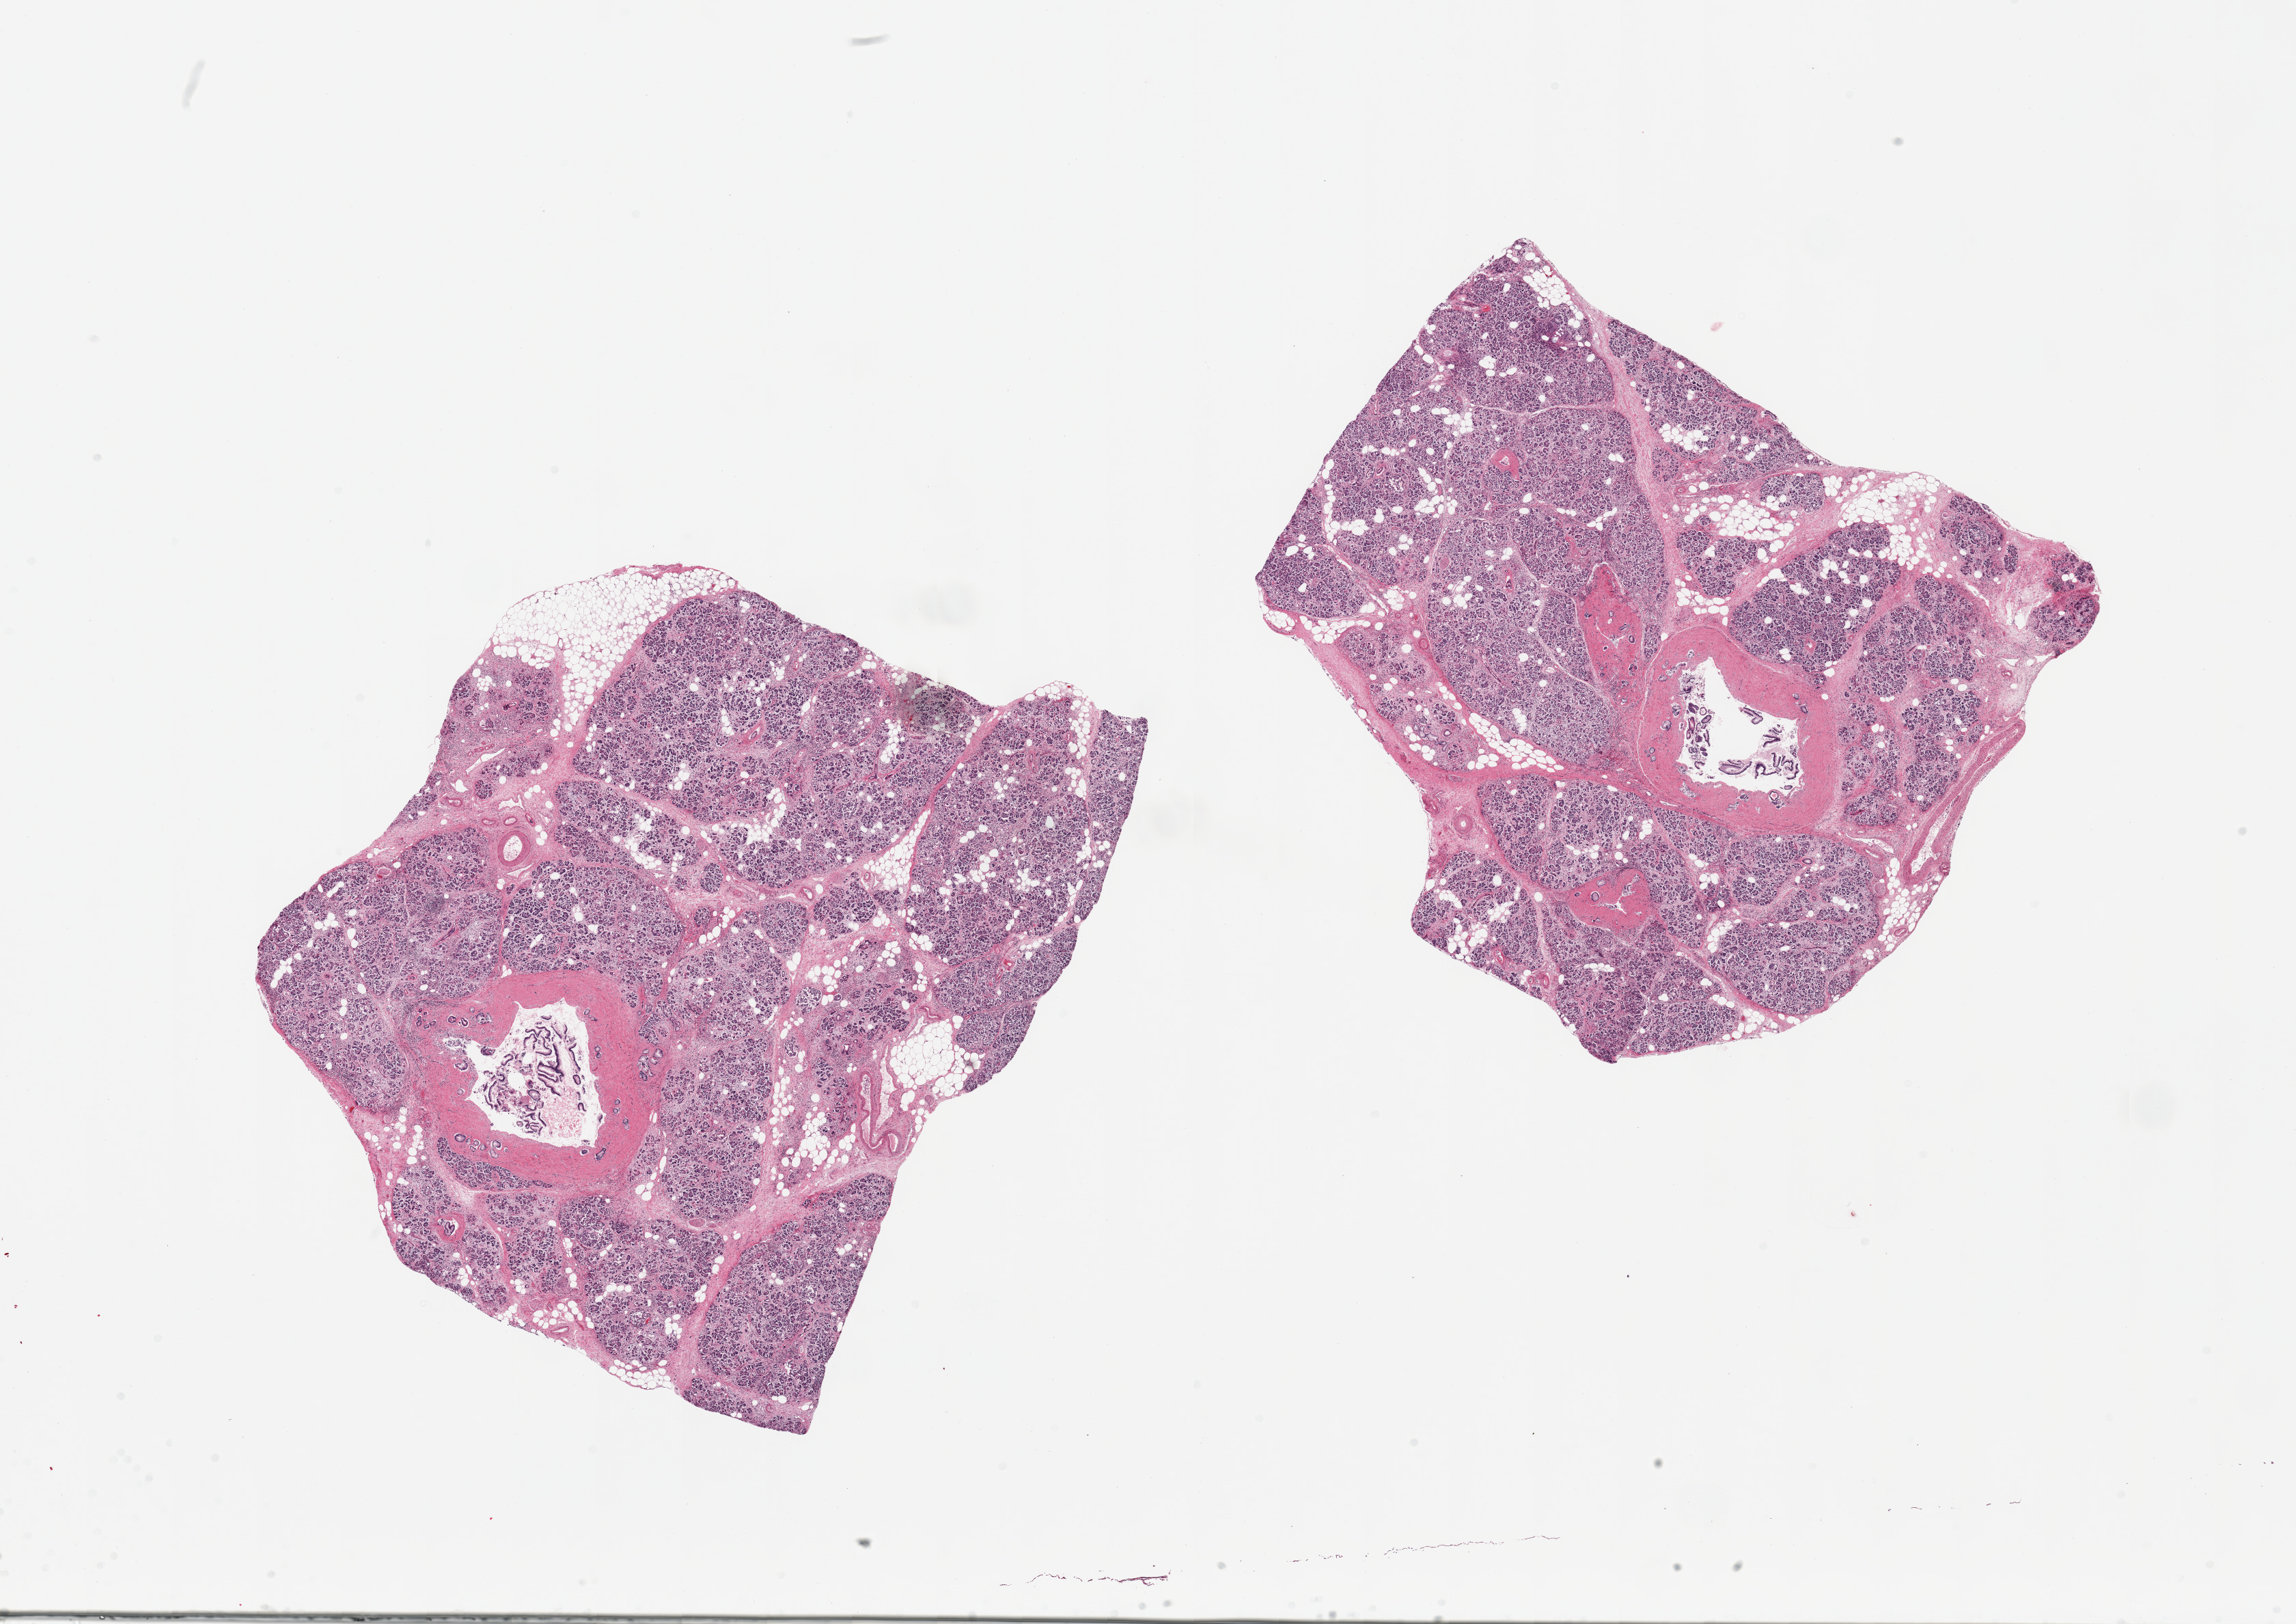
Digitized H&E-stained section, brightfield — whole scanned area (about 26.6 x 18.8 mm) shown as a low-resolution overview, PAXgene-fixed paraffin-embedded (PFPE) section, target tissue: pancreas, tissue donor sample. Female donor.
Review note (as recorded): 2 pieces, advanced saponification/autolysis.